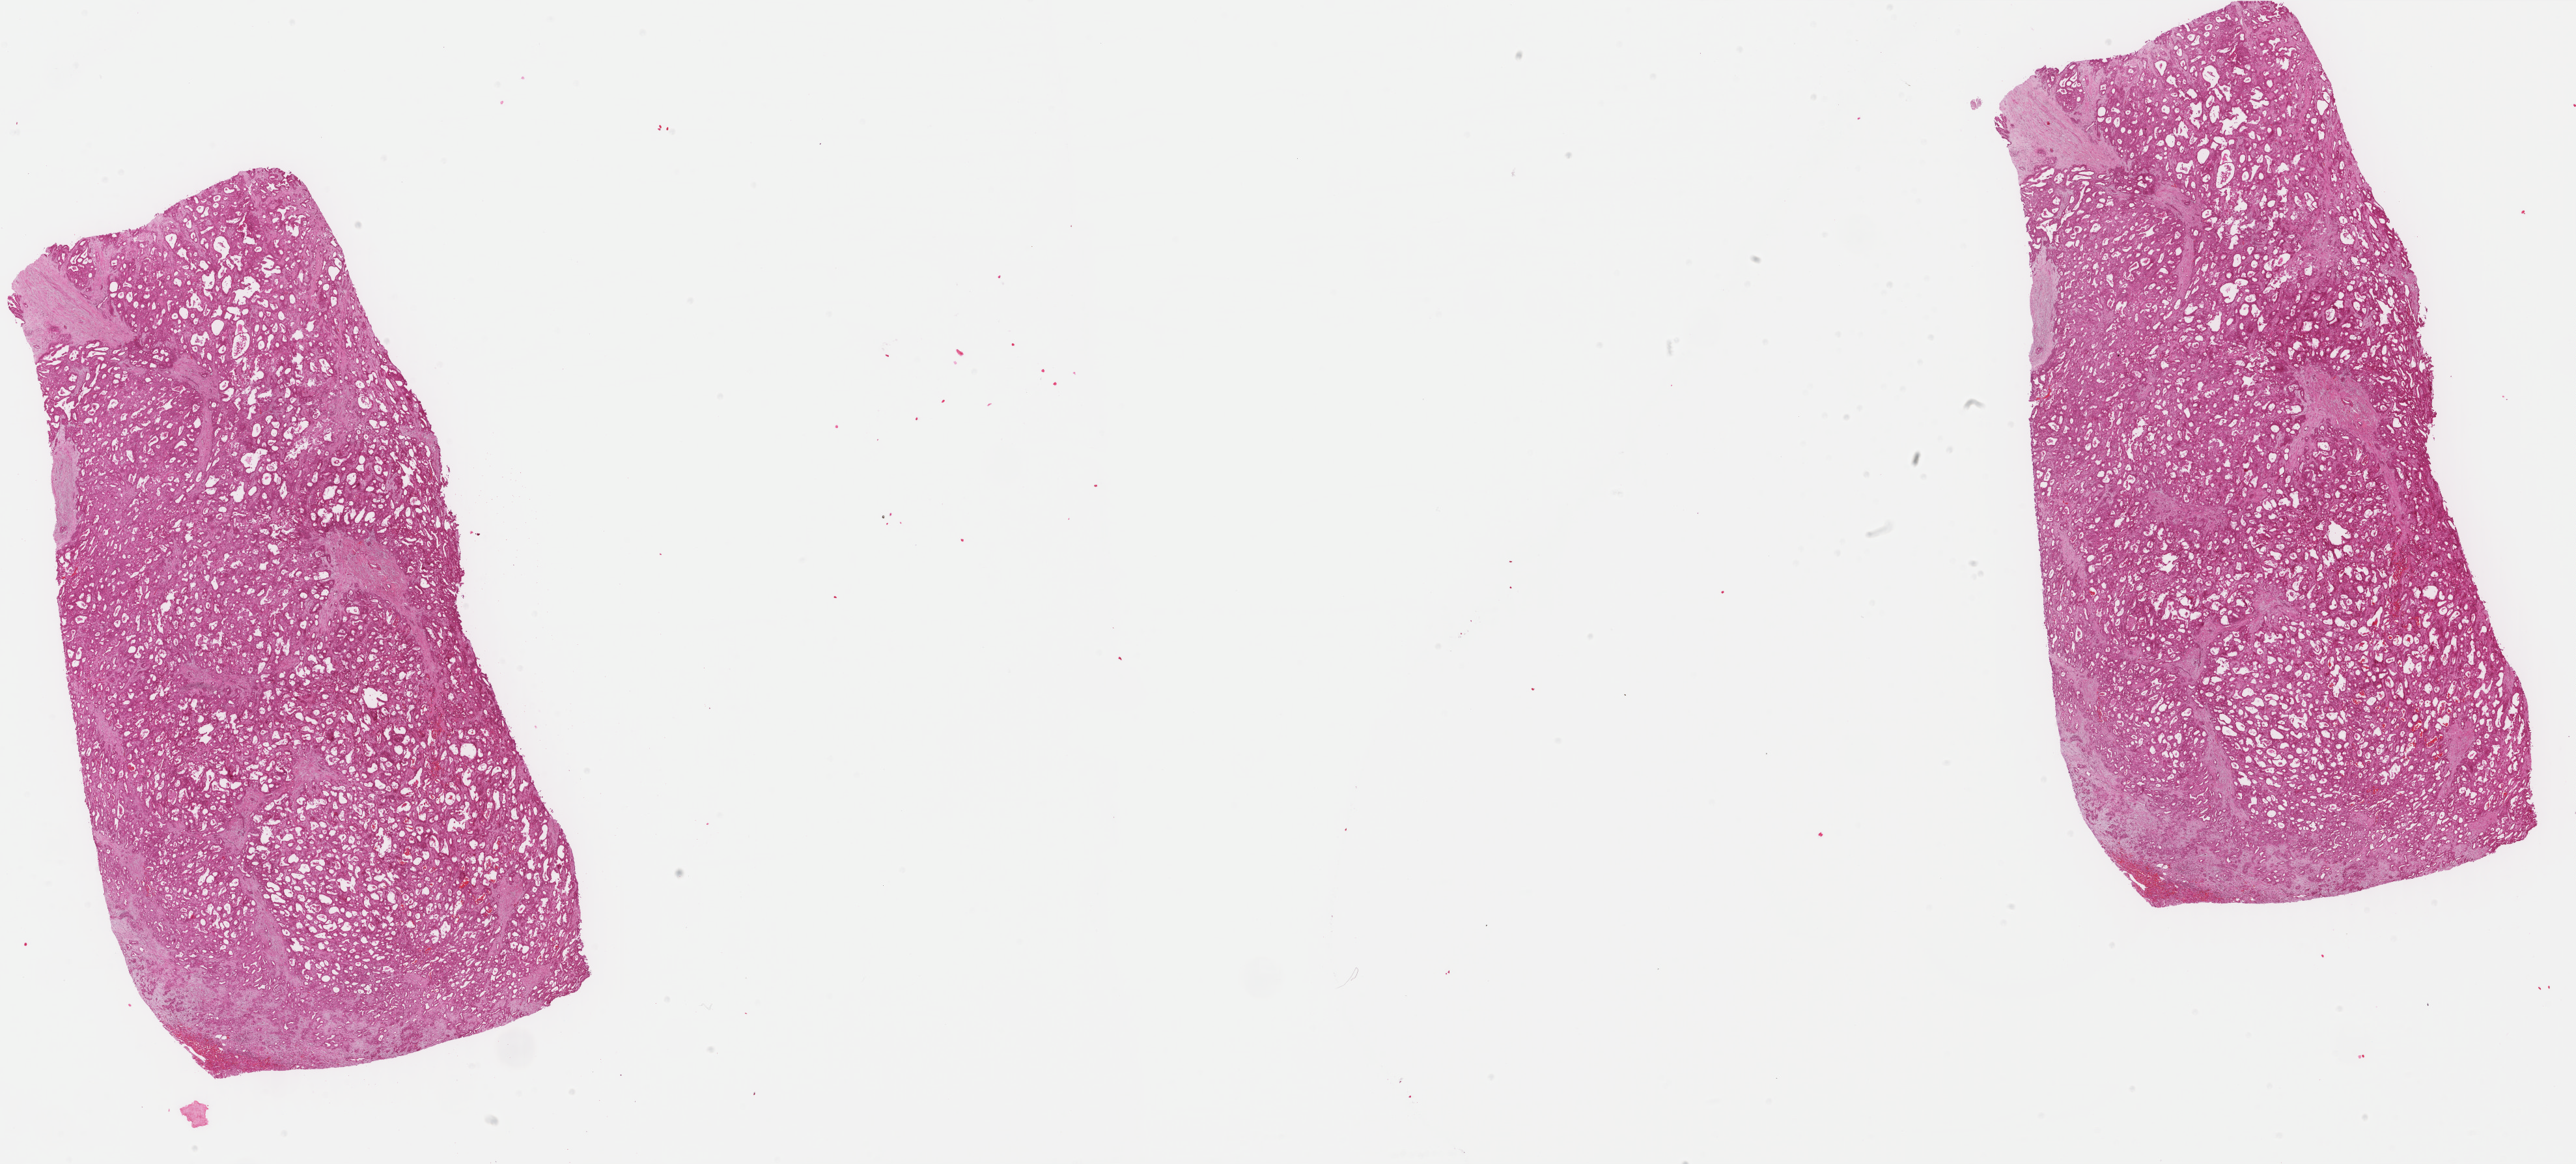
Digitized H&E tissue section (whole slide) — whole scanned area (about 31.4 x 14.2 mm, from a 40x scan) shown as a low-resolution overview, FFPE section, liver, primary tumour sample. Female patient; age at initial diagnosis 72 years.
- histologic diagnosis: Hepatocellular carcinoma, NOS